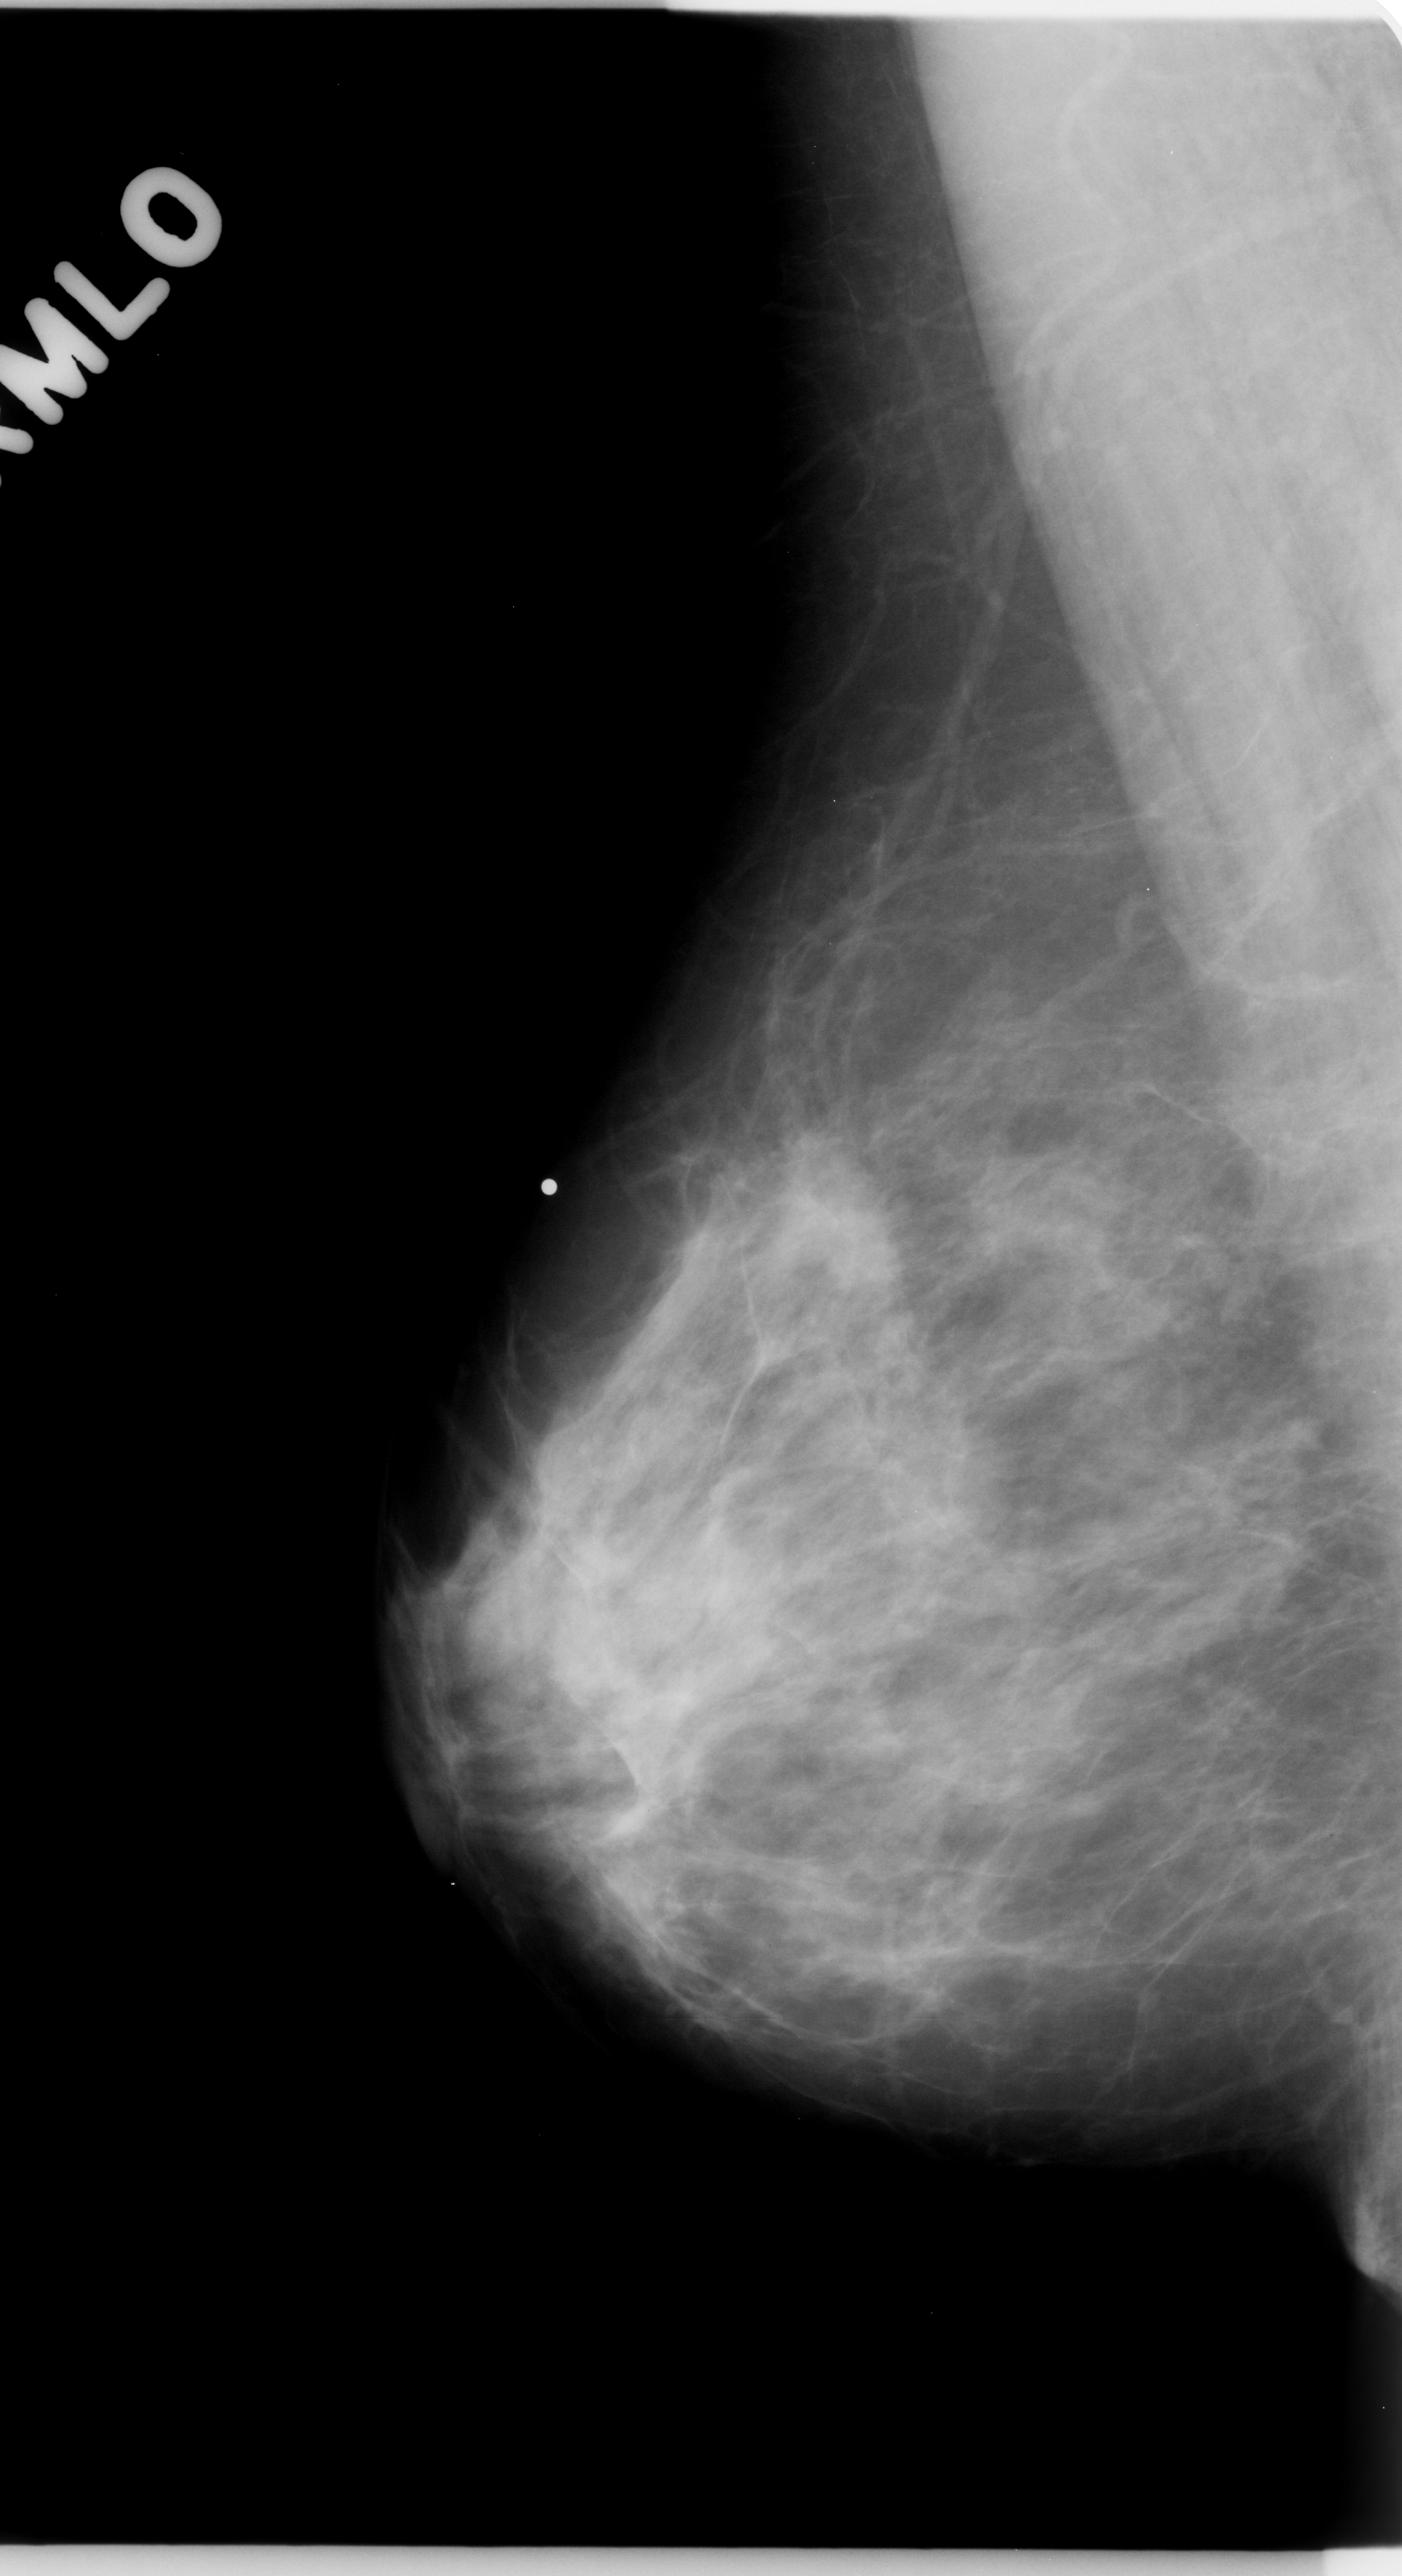
Mammogram (digitized film); right breast; MLO view; BI-RADS breast density category 2 (scale 1–4).
Finding: mass, shape irregular, margins spiculated; BI-RADS assessment category 5; pathology result (as recorded, not read from the image): malignant.